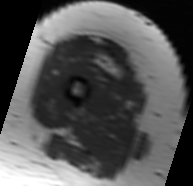
MRI of an extremity soft-tissue mass, one axial slice. Position 18 of 91 along the scan axis. MR volume resampled by the dataset authors to the PET/CT grid (not the native acquisition matrix). 193 × 186 image matrix, field of view 188 × 182 mm. Female patient. Case-level facts recorded for this patient, not image findings: histological type: malignant solitary fibrous tumor; grade: intermediate; site of the primary tumour: right thigh.
Structures marked on this image (expert contour drawn on MRI and transferred to this co-registered scan by the dataset authors):
- gross tumour volume including surrounding oedema: bounding box [x1, y1, x2, y2] px = [70, 37, 128, 79]